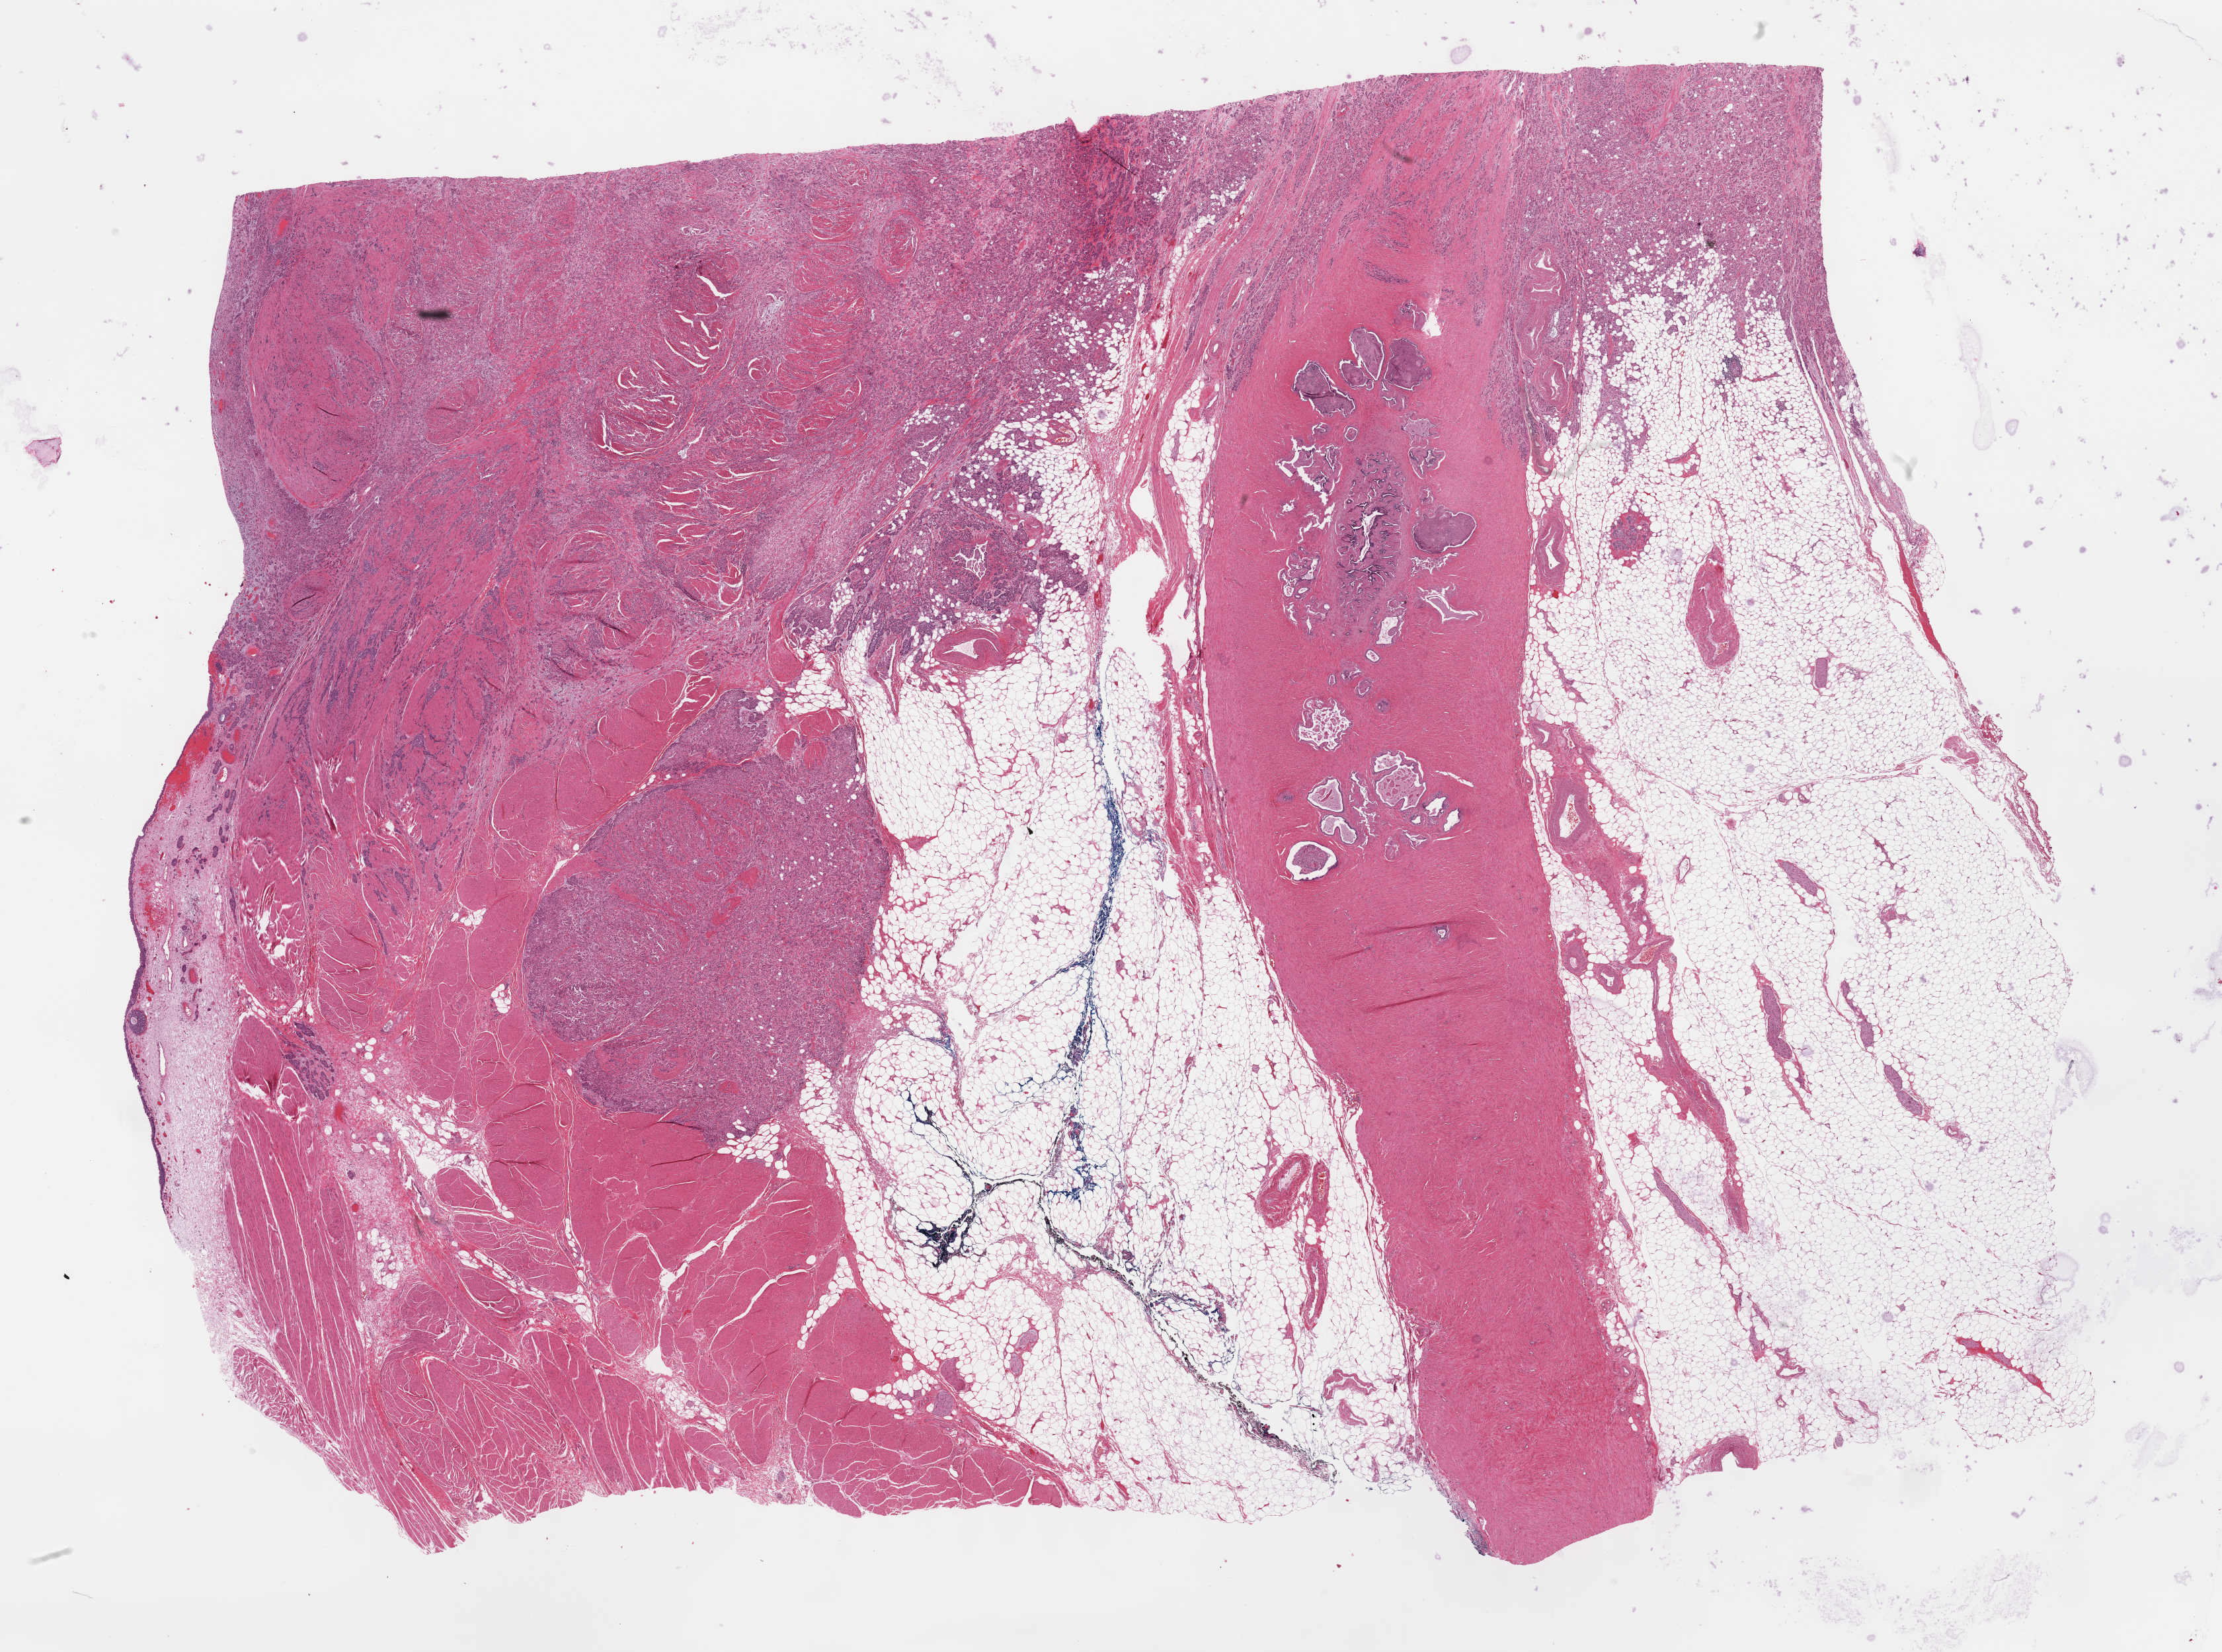
Hematoxylin and eosin (H&E) stained whole-slide image, a low-resolution overview of the entire scanned area, about 27.2 x 20.2 mm. FFPE section. Bladder, primary tumour sample. Patient: male, age at initial diagnosis 73 years. Histologic grade: high grade.
• AJCC pathologic stage: IV (7th edition)
• pathologic diagnosis: Transitional cell carcinoma
• lymph nodes positive (case pathology): 1 of 21 examined